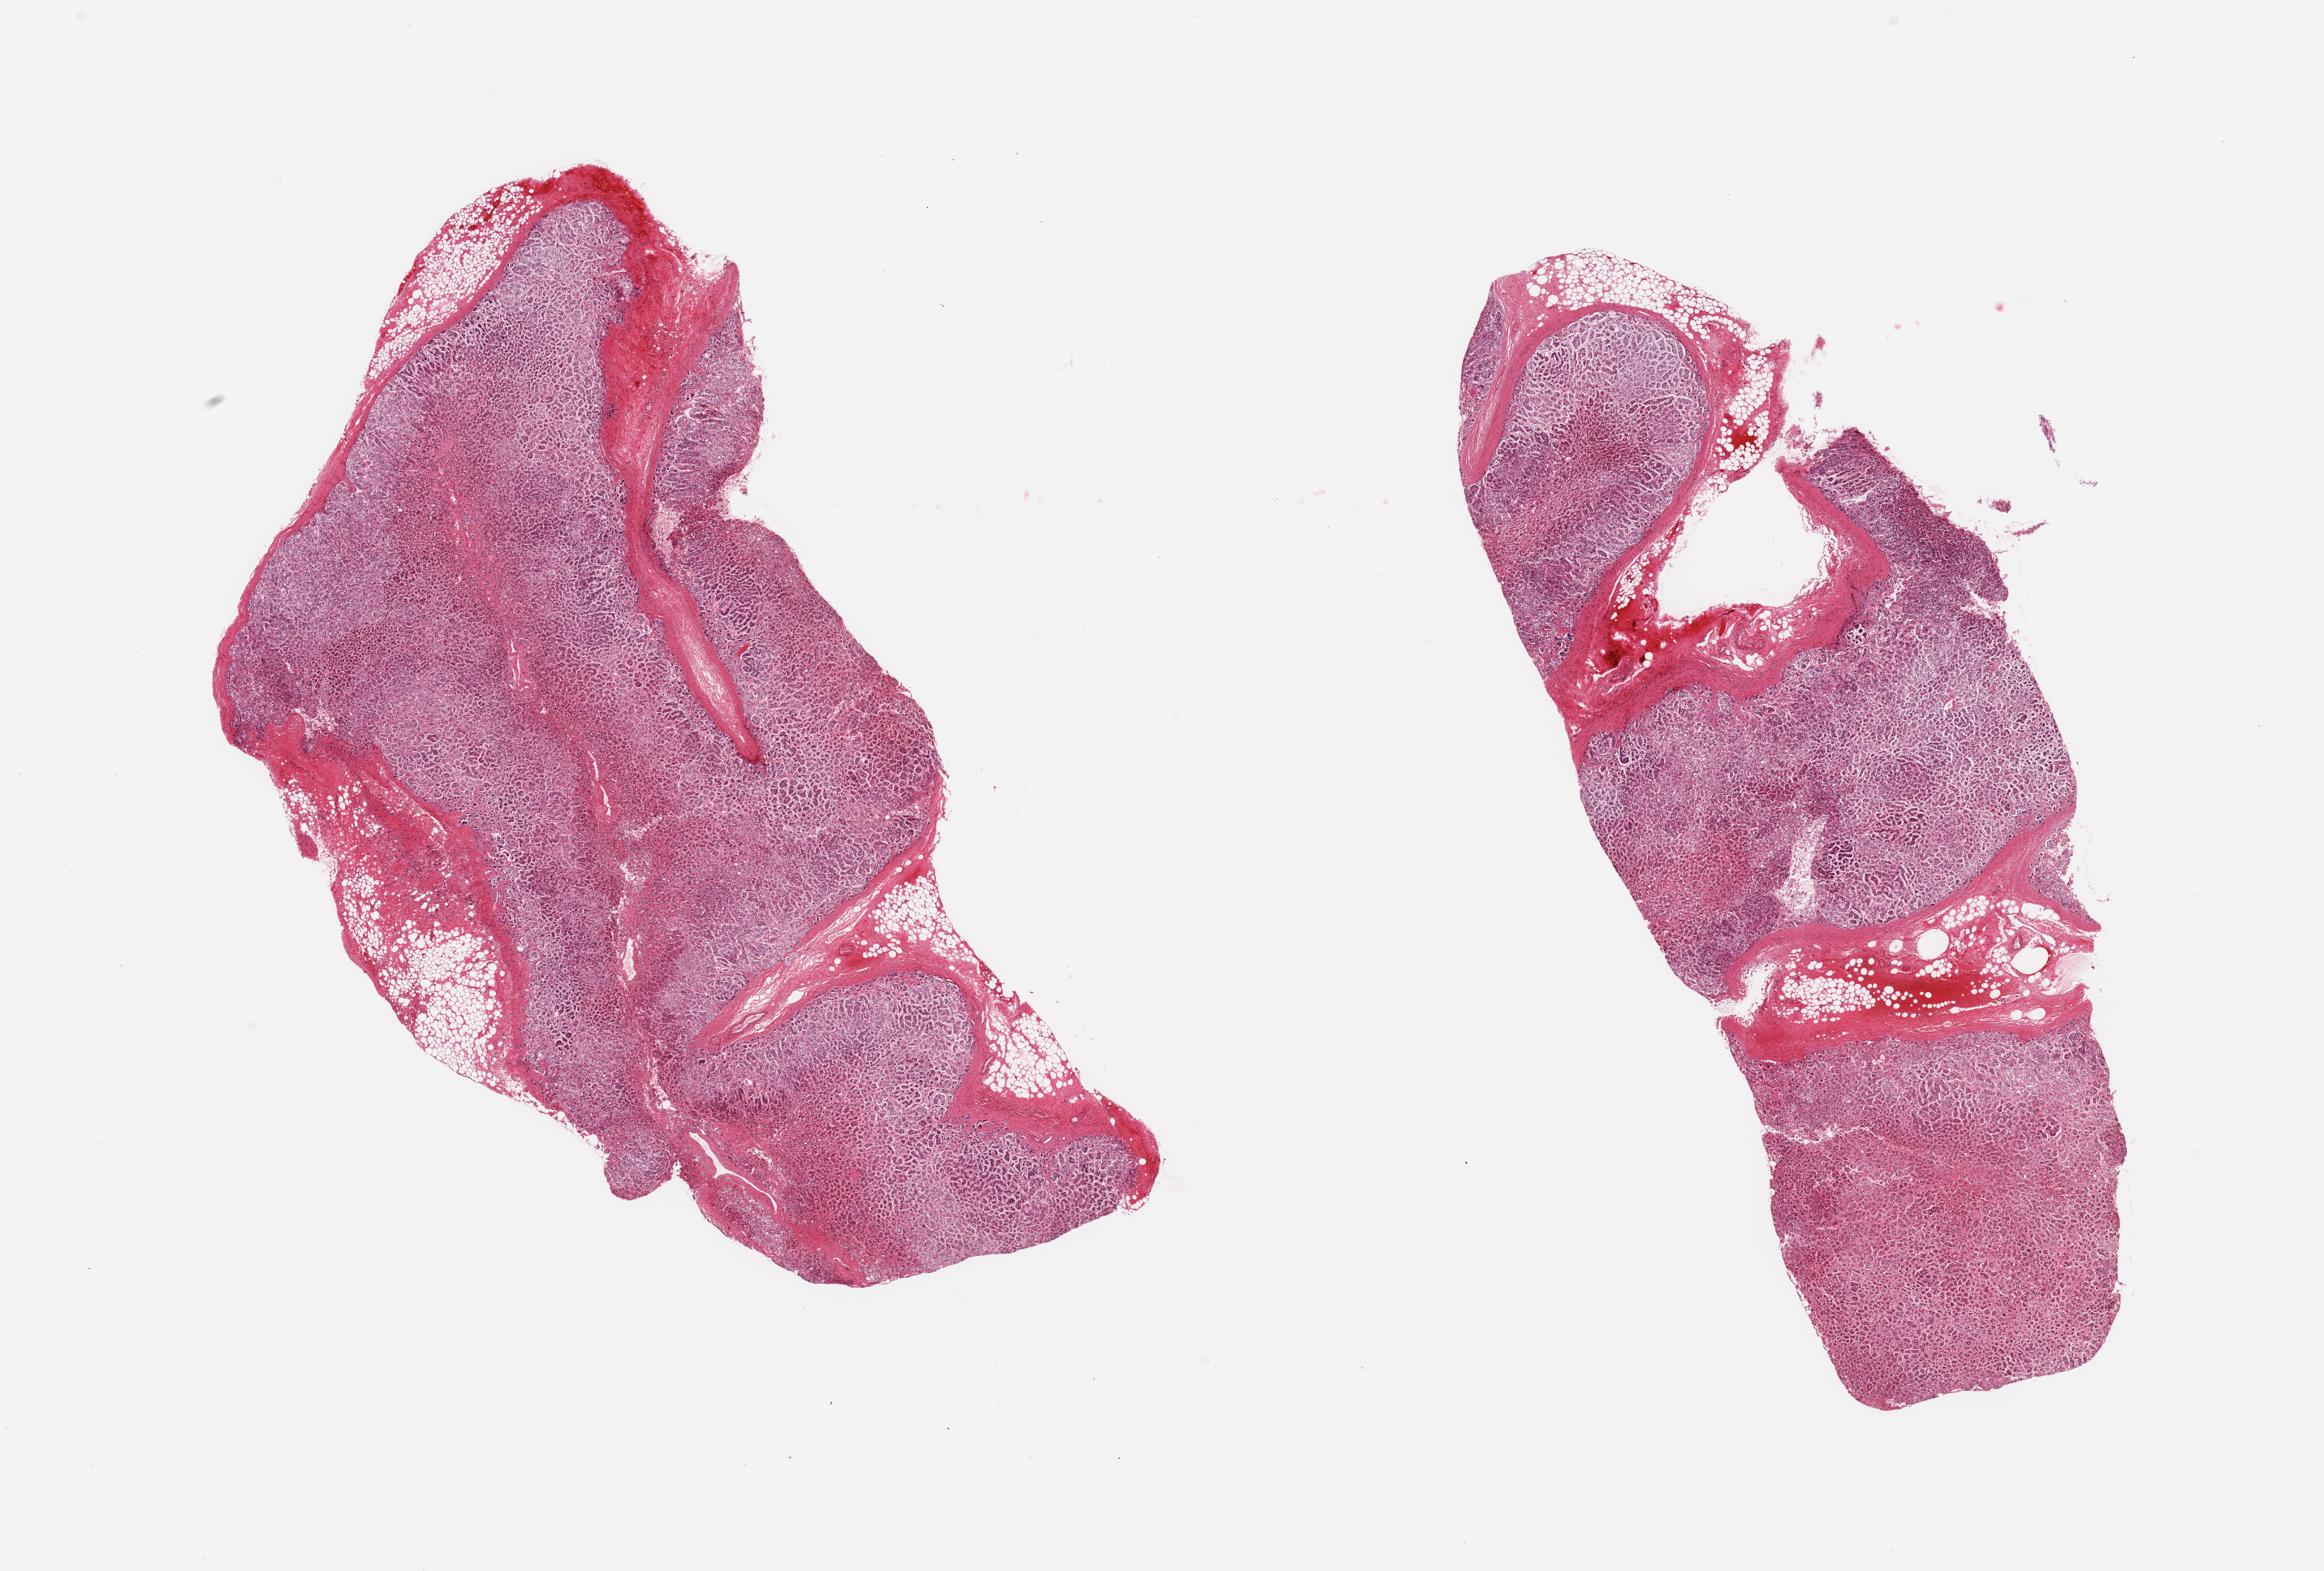
Haematoxylin and eosin whole-slide image, brightfield — whole scanned area (about 22.6 x 15.3 mm, slide scanned at 20x) shown as a low-resolution overview; PAXgene-fixed, paraffin-embedded tissue; section of adrenal gland (target tissue); donor tissue sample. Male donor.
* reviewer comment on this tissue sample: 2 pieces; 10% faat content